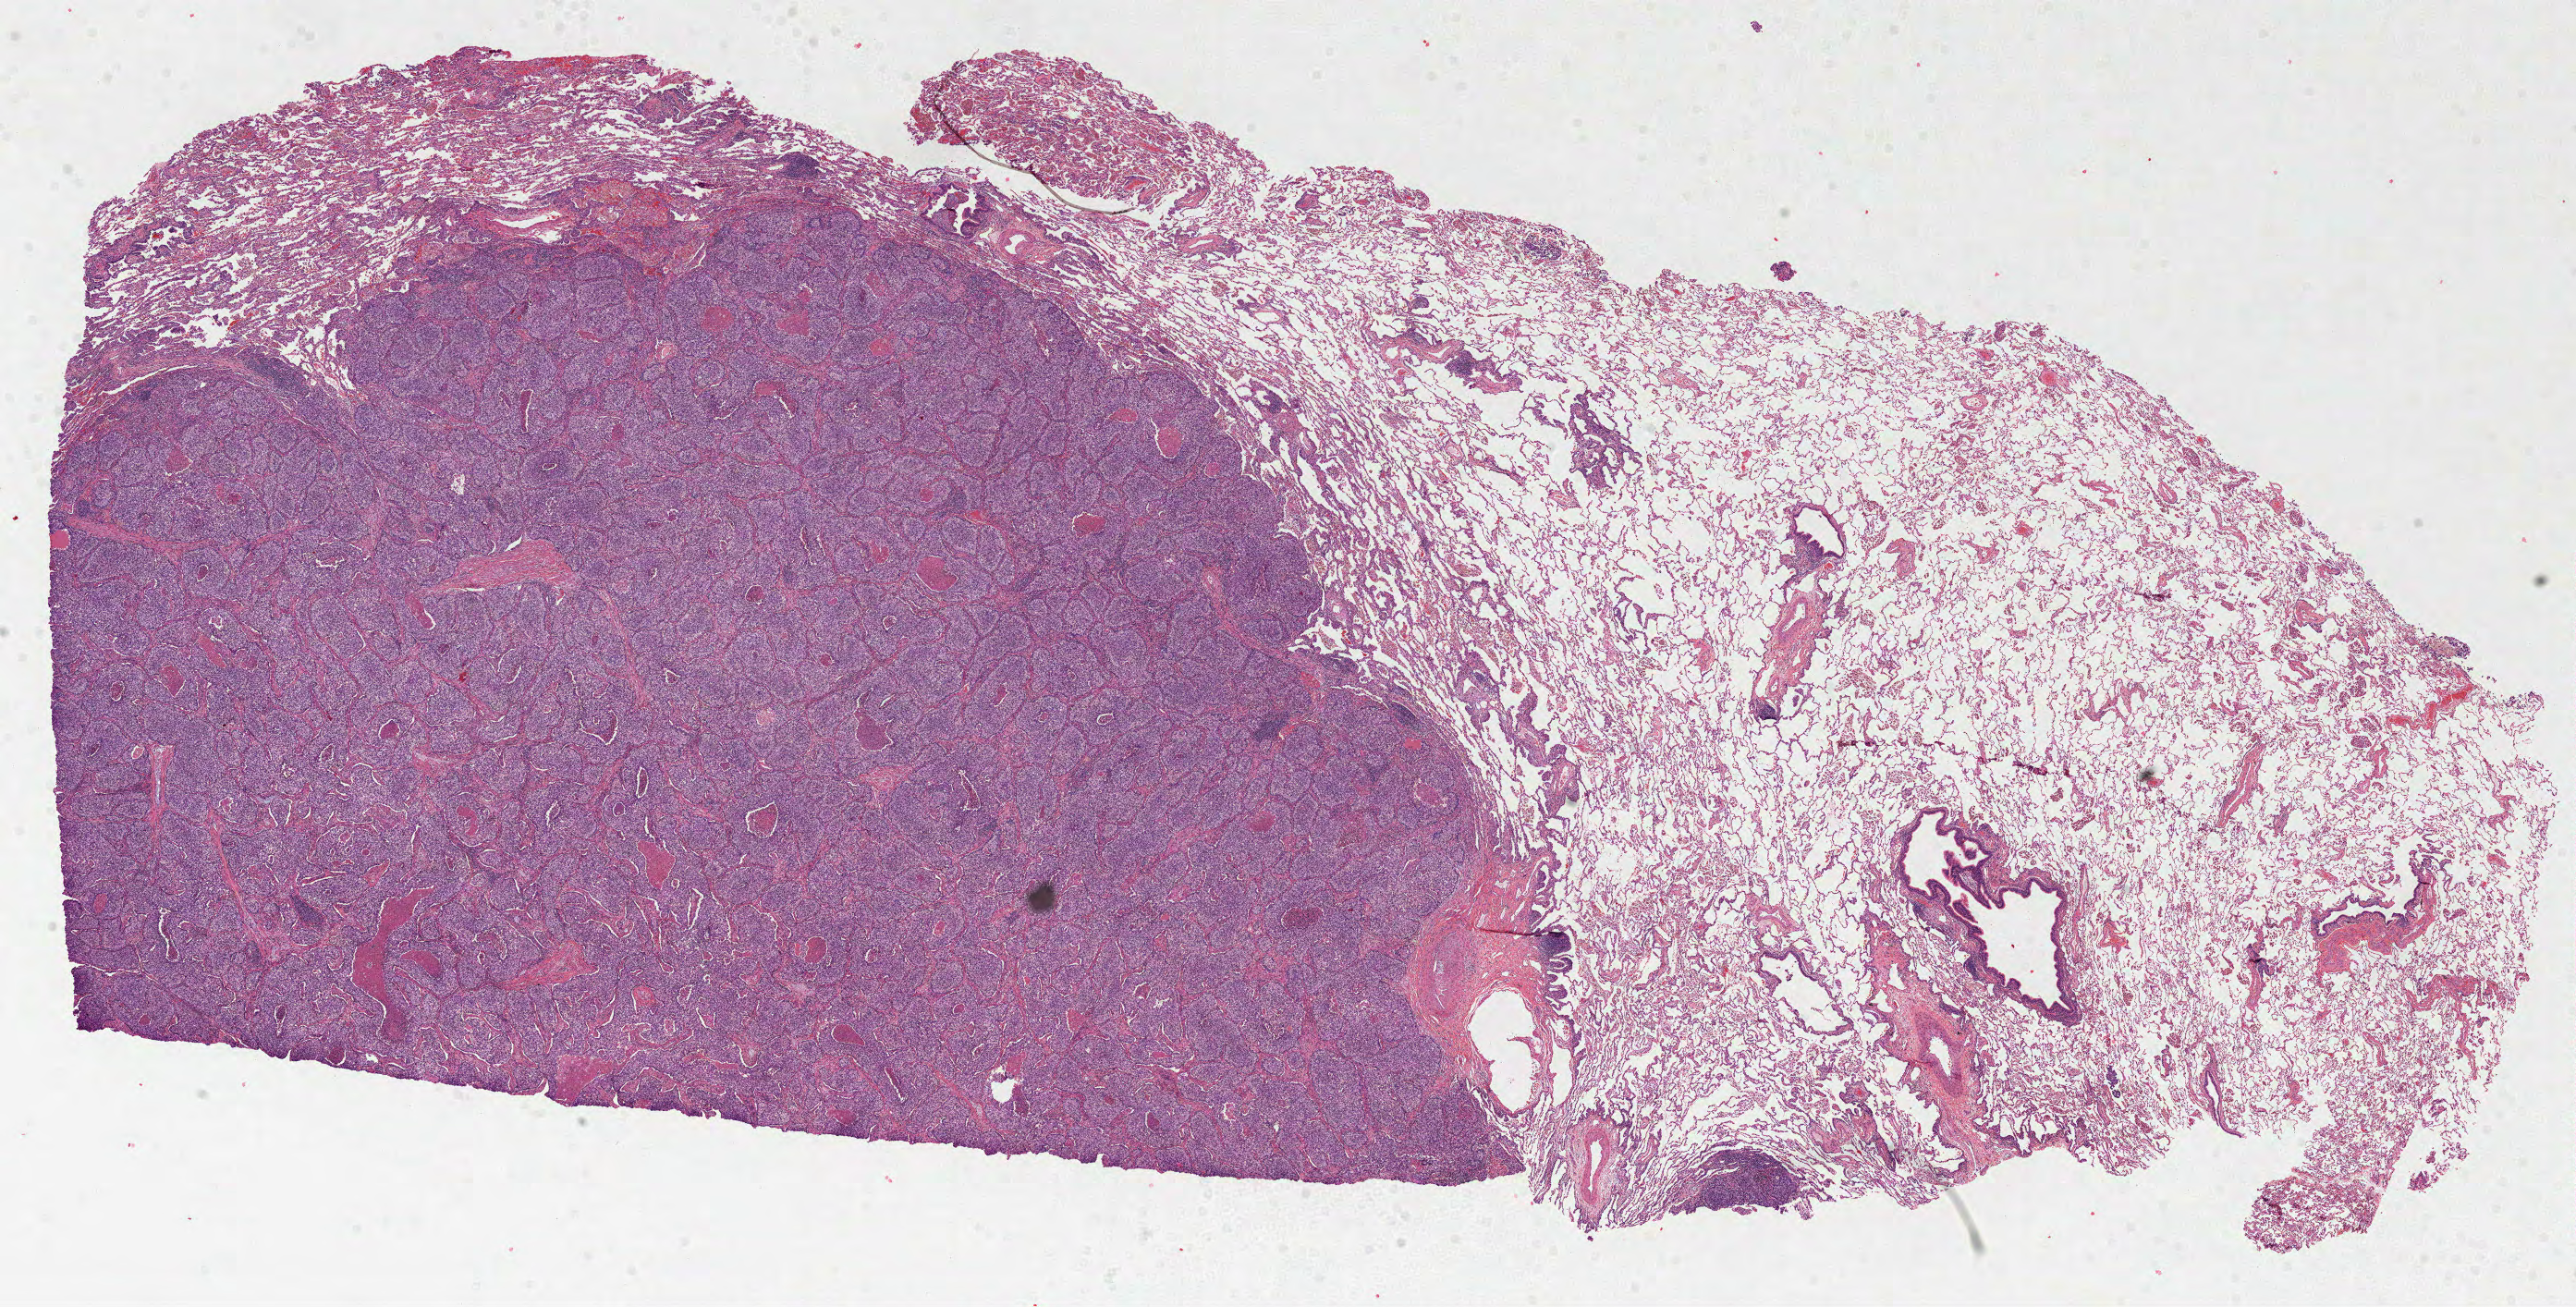
Whole-slide histology image, H&E — a low-resolution overview of the entire scanned area, about 22.5 x 11.4 mm (acquisition: 40x scan); FFPE section; primary tumour sample from the lung. Female, age 42 years at initial diagnosis.
Histologic diagnosis: Adenocarcinoma with mixed subtypes (middle lobe, lung).